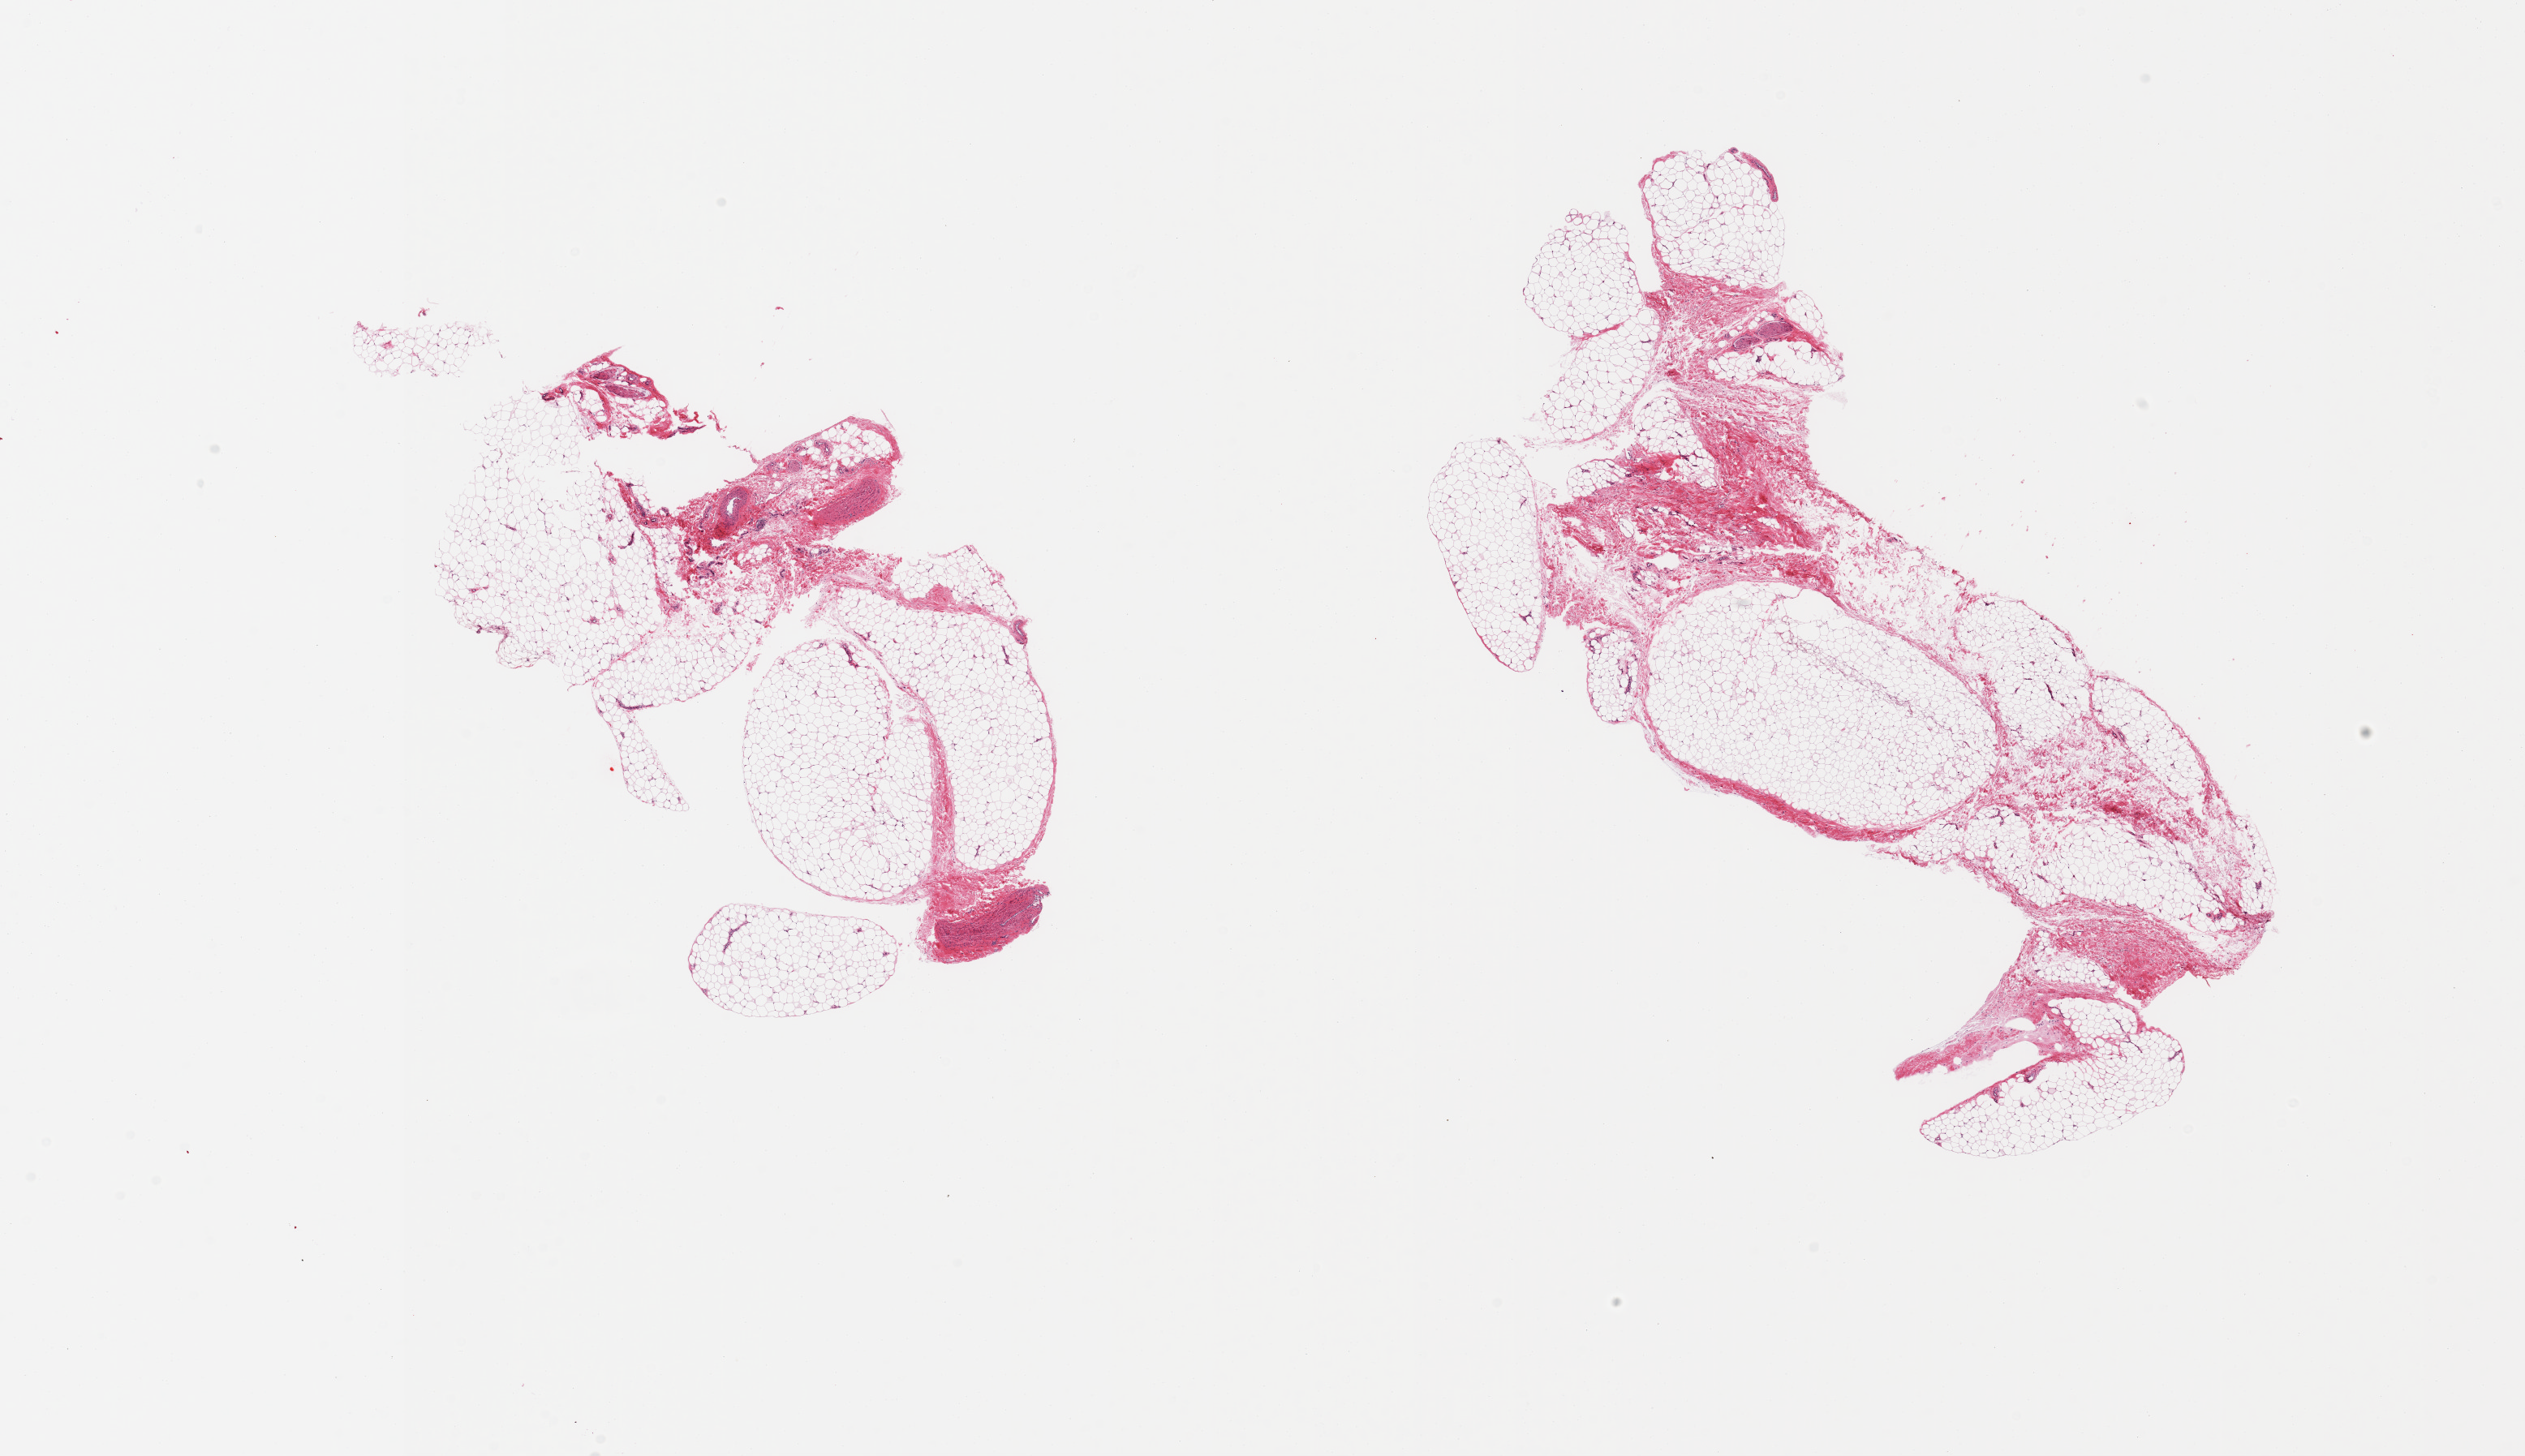
Digitized haematoxylin and eosin-stained section, brightfield, shown as a low-resolution overview of the whole scanned area (about 24.6 x 14.2 mm). PAXgene-fixed paraffin-embedded (PFPE) section. Sampled site (target tissue): adipose tissue. Donor tissue sample.
Pathologist's review note for this sample: 2 pieces; mature adipose tissue and fibrovascular component.